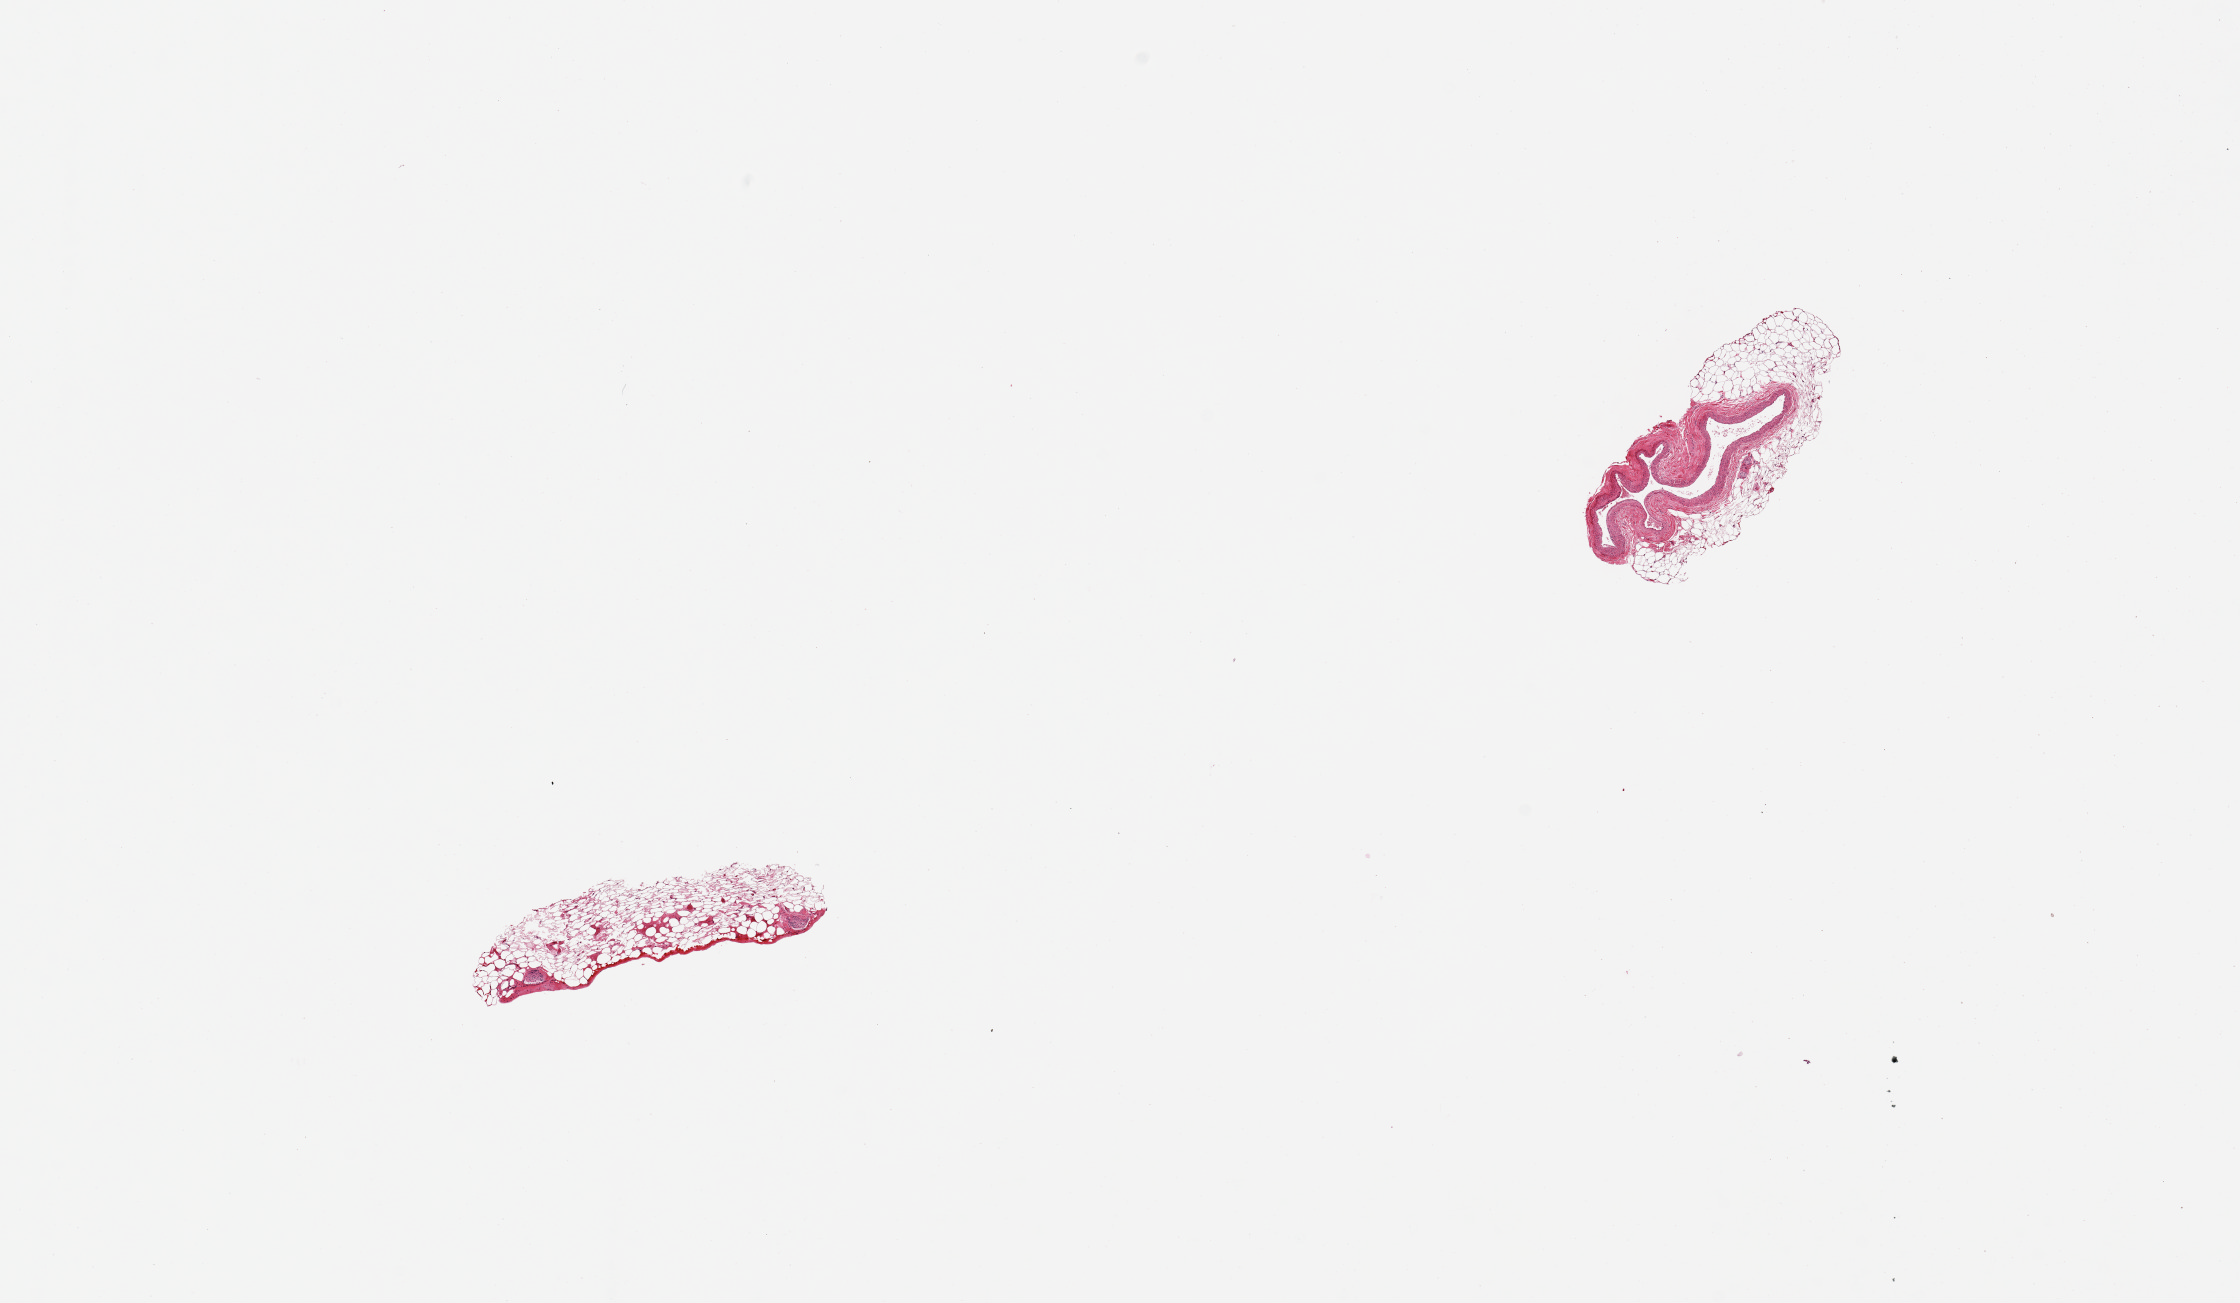
Digitized haematoxylin and eosin-stained section, brightfield, a low-resolution overview of the entire scanned area, about 17.7 x 10.3 mm, PAXgene-fixed paraffin-embedded (PFPE) section, sampled site (target tissue): coronary artery, tissue donor sample. Donor sex: female.
Review note (as recorded): 2 pieces, one all fat, the other vessel with adherent fatty nubbin, fat.